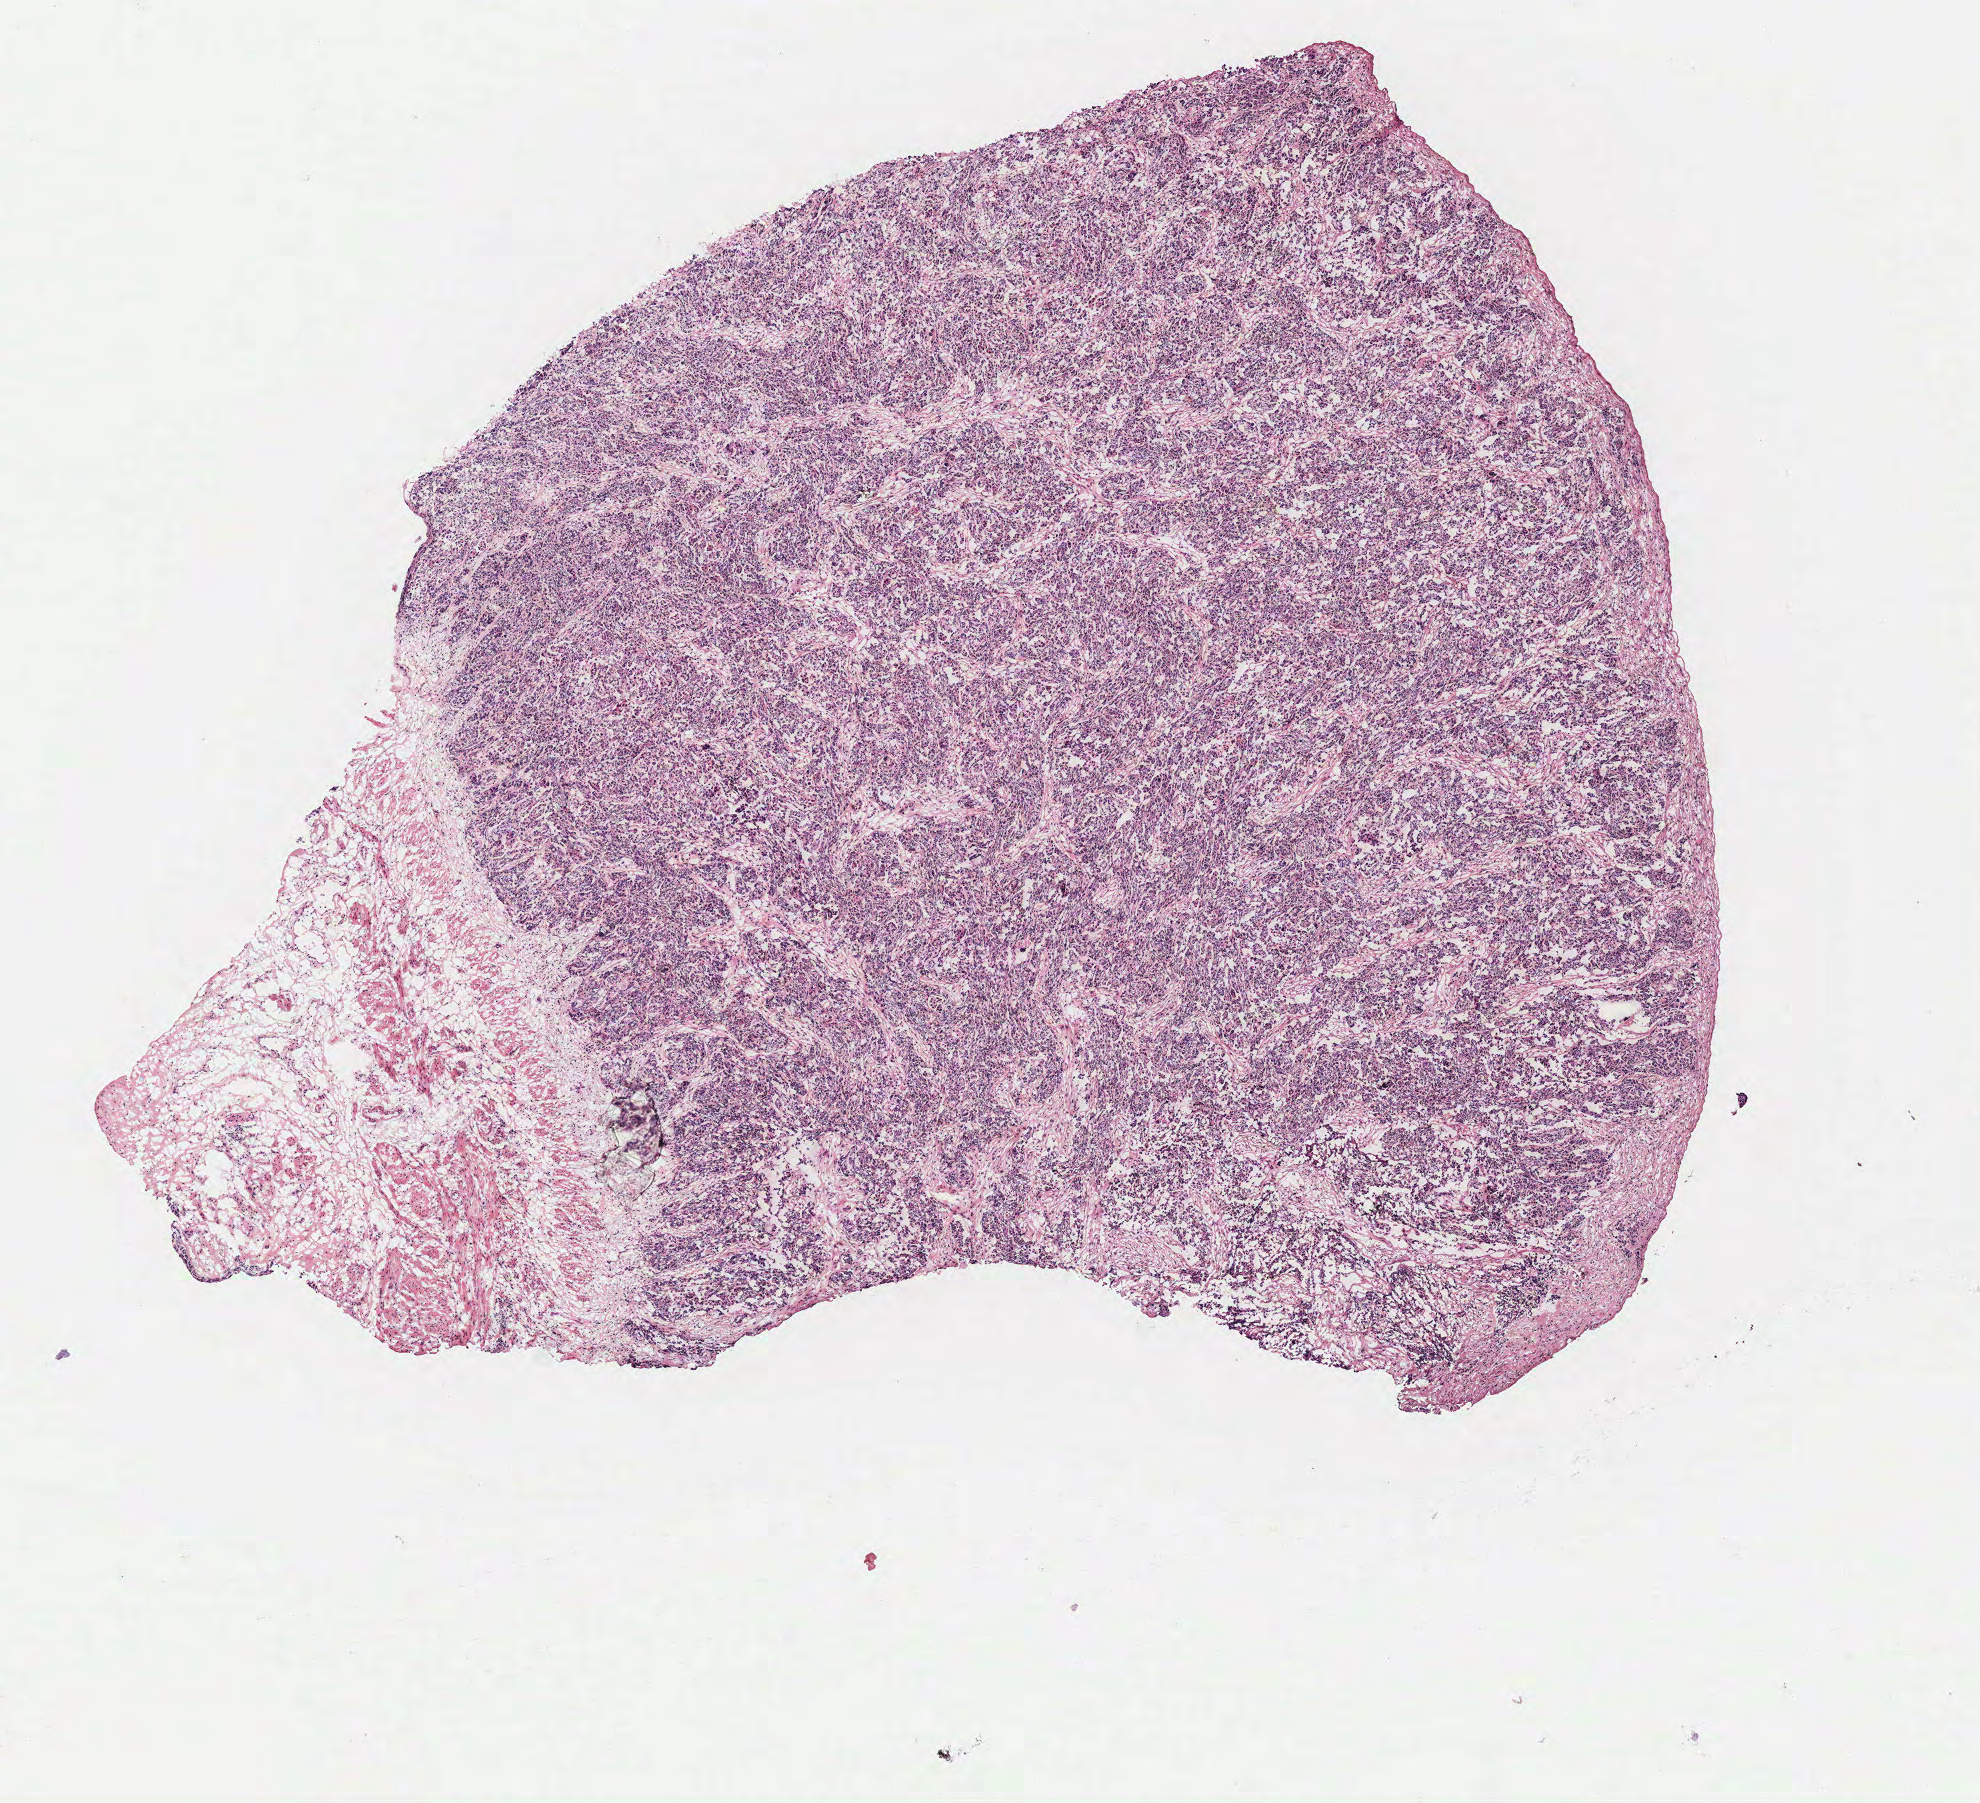
Digitized Hematoxylin and eosin (H&E) stained tissue section (whole slide), low-resolution overview of the scanned area, about 7.9 x 7.2 mm (slide scanned at 40x), ovary, tissue type not recorded. Patient sex: female.
* patient diagnosis: Serous adenocarcinoma, NOS